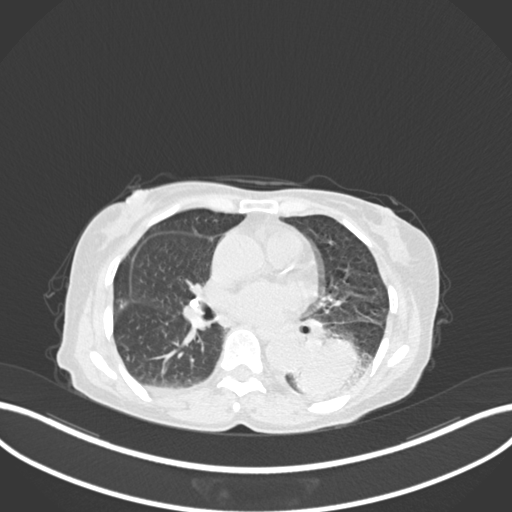
Chest CT, one axial slice; slice 78 of 233 in the series (ordered by position); reconstruction kernel B30f; 120 kVp; lung window (W 1500 / L -600 HU); 512 × 512 image matrix, field of view 400 × 400 mm. Female patient, age 78 years. Case-level facts recorded for this patient, not image findings: clinical TNM (as recorded): T3 N0 M1.
Structures marked on this image (rectangle marked by the reading radiologist):
- lung tumour (recorded histology: squamous cell carcinoma): bounding box (x1, y1, x2, y2) in pixels: (287, 328, 360, 400)